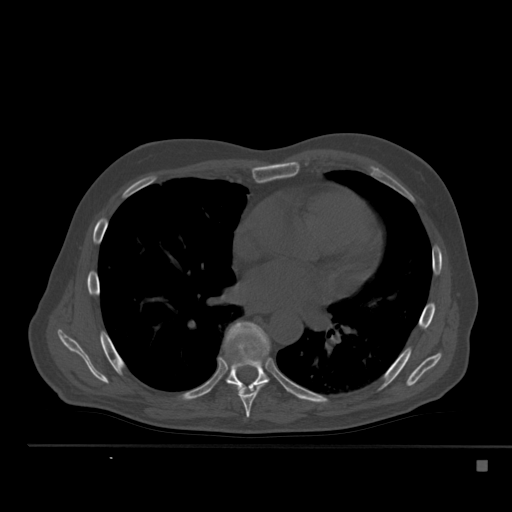
CT including the spine, one axial slice; slice 318 of 517 in the series (ordered by position); reconstruction kernel Br40s; 120 kVp; bone window (W 1800 / L 400 HU); 1.5 mm slice thickness; 512 × 512 image matrix, field of view 408 × 408 mm. Male patient, age 70 years. Case-level facts recorded for this patient, not image findings: primary cancer: renal; vertebrae with lytic lesions (as recorded): T4, T6, T10, T12, L3, L4, L5.
Annotated regions visible in this slice (semi-automatic segmentation, software-assisted and operator-edited):
- T7 vertebra: bounding box <228,365,267,418> (left, top, right, bottom; pixels)
- T8 vertebra: <224,321,270,393>